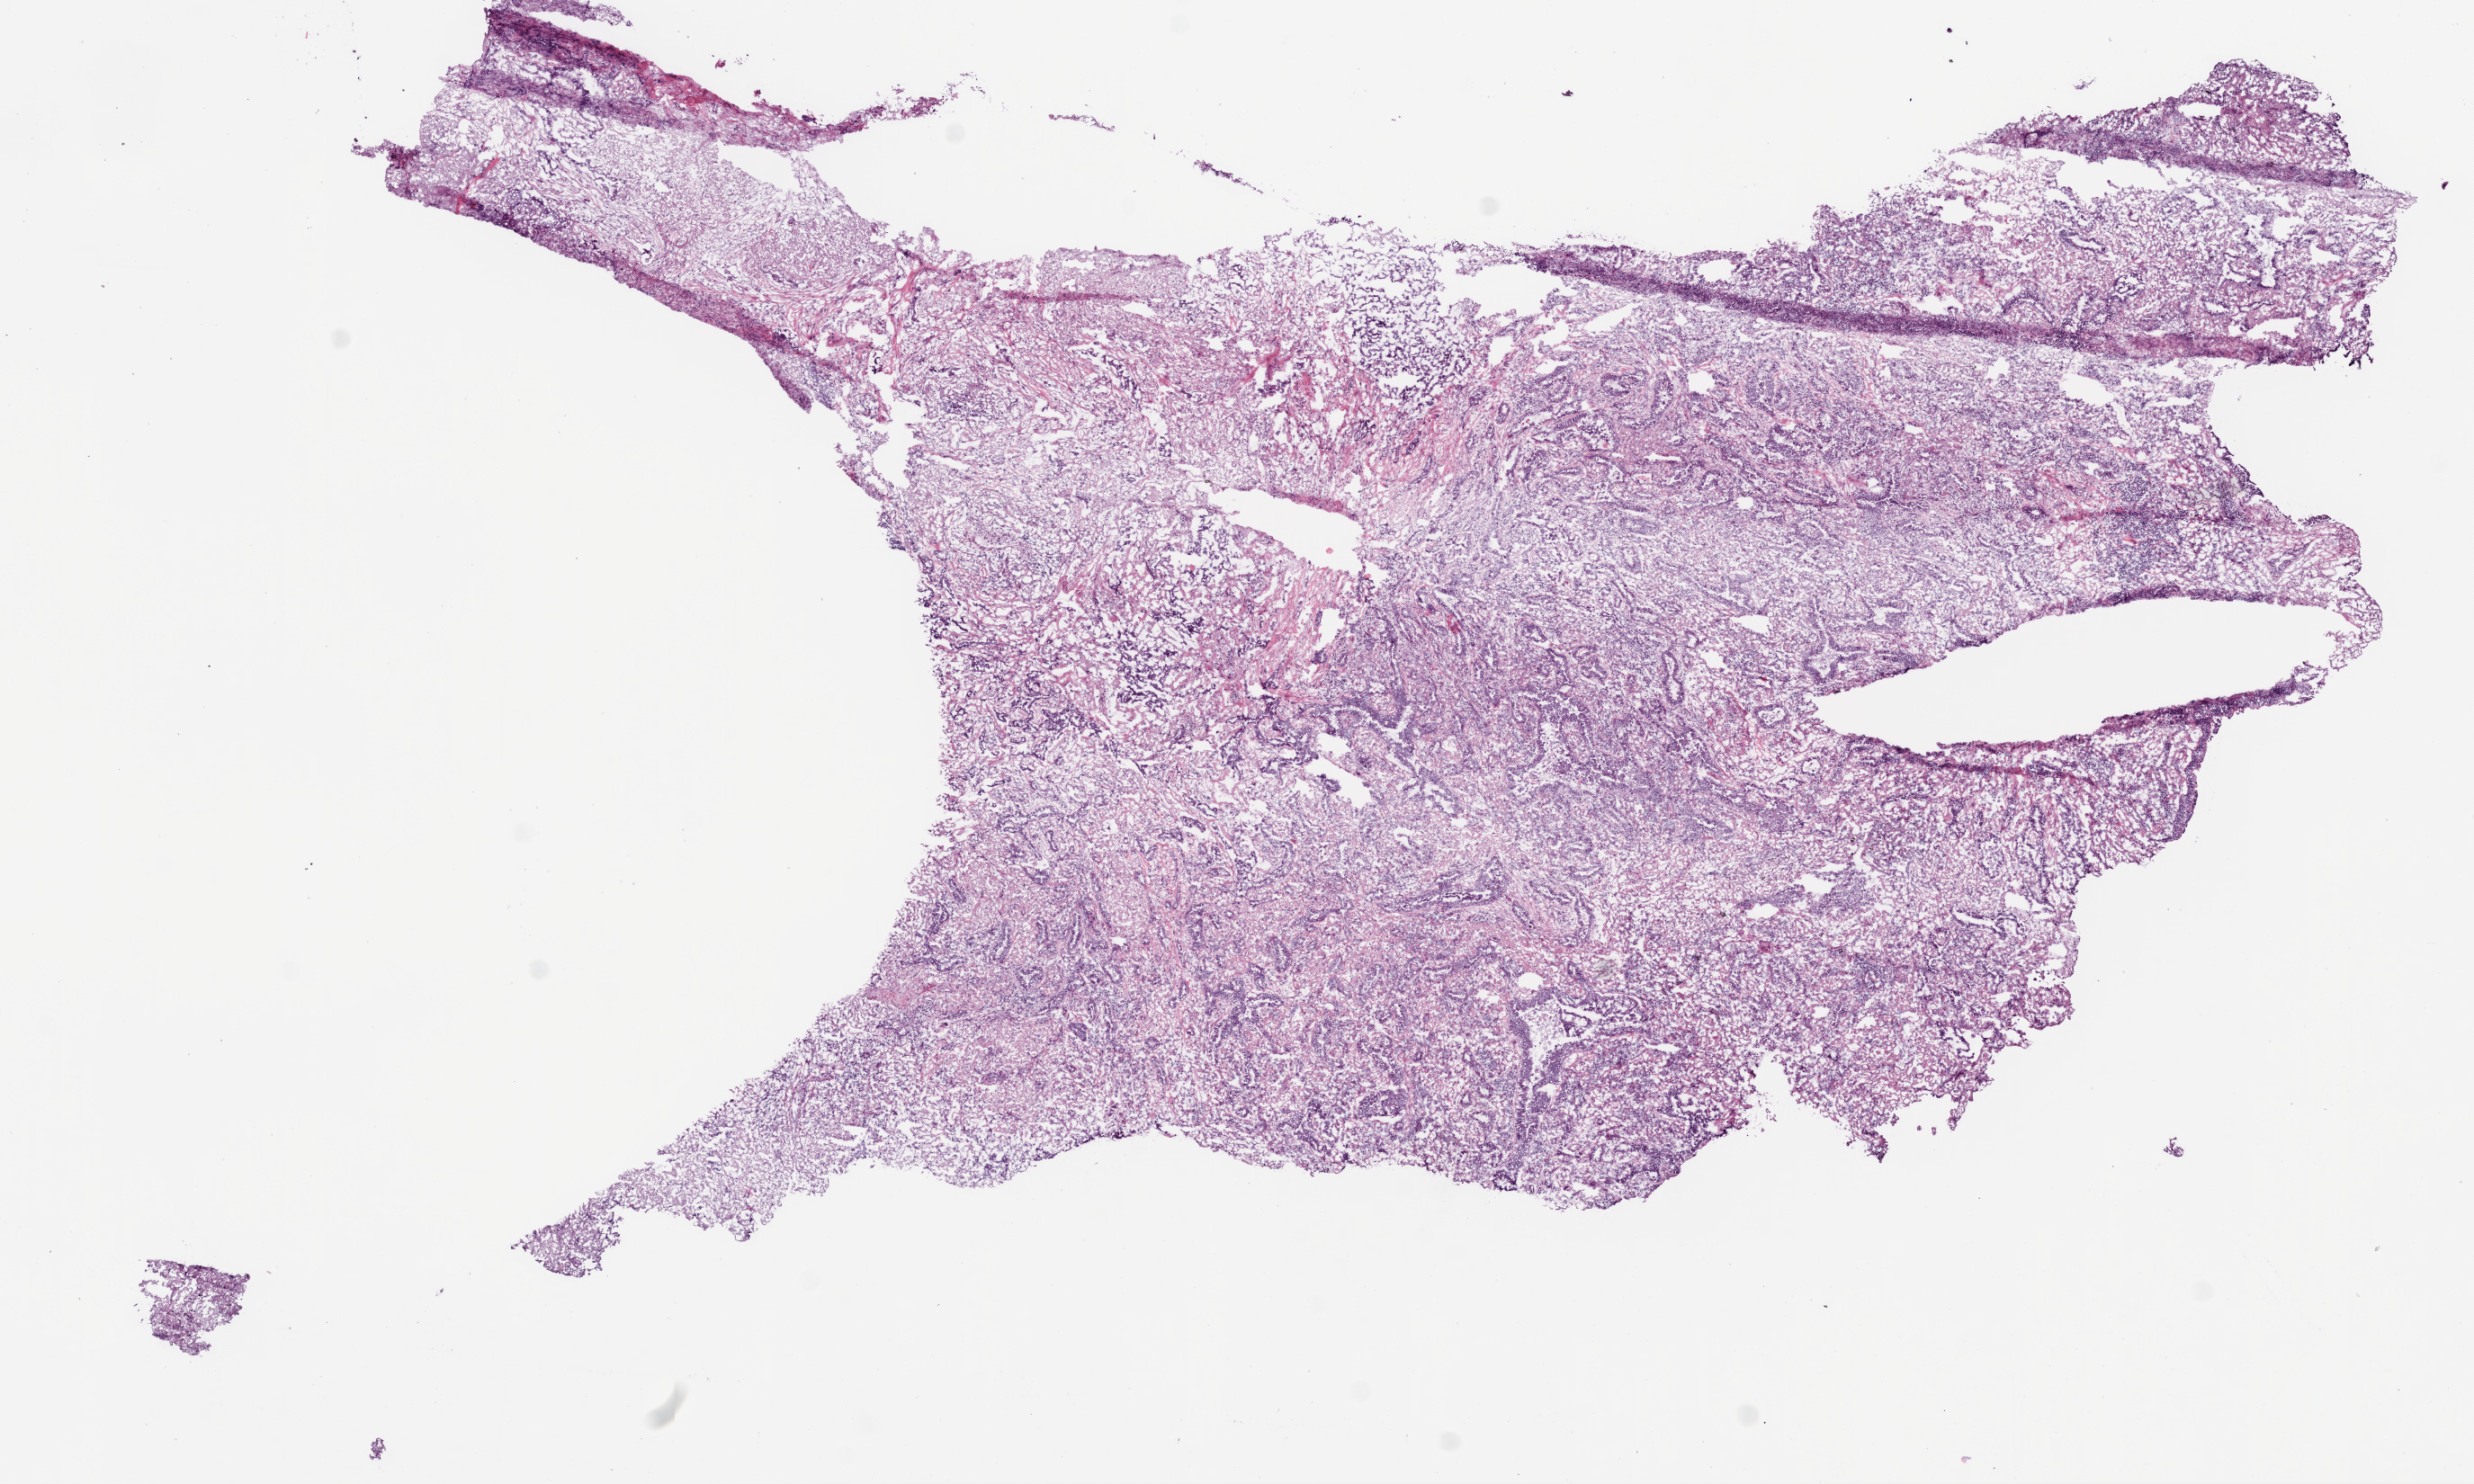
Whole-slide histology image, H&E-stained, a low-resolution overview of the entire scanned area, about 11.0 x 6.6 mm, frozen section, lung, primary tumour sample. Patient: female, age at initial diagnosis 82 years. Composition of this section per pathologist review: tumour cells 80%, tumour nuclei 75%, normal cells 0%, stromal cells 15%, necrosis 5%.
AJCC pathologic stage: IB (6th edition). Laterality: right. Histologic diagnosis: Adenocarcinoma, NOS (upper lobe, lung).